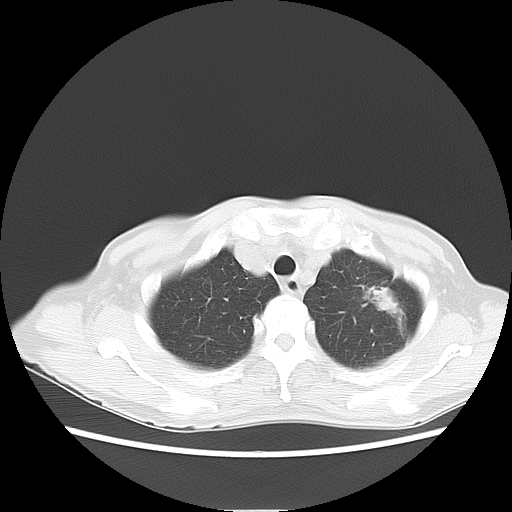
Chest CT, one axial slice. Slice 11 of 13 in the series (ordered by position). Reconstruction kernel LUNG. Lung window (W 1500 / L -600 HU). 512 × 512 image matrix. Patient: female, 71 years. Case-level facts recorded for this patient, not image findings: clinical TNM (as recorded): T2 N0 M0.
Outlined on this slice (rectangle marked by the reading radiologist):
- lung tumour (recorded histology: adenocarcinoma): bounding box <360,283,404,321> (left, top, right, bottom; pixels)